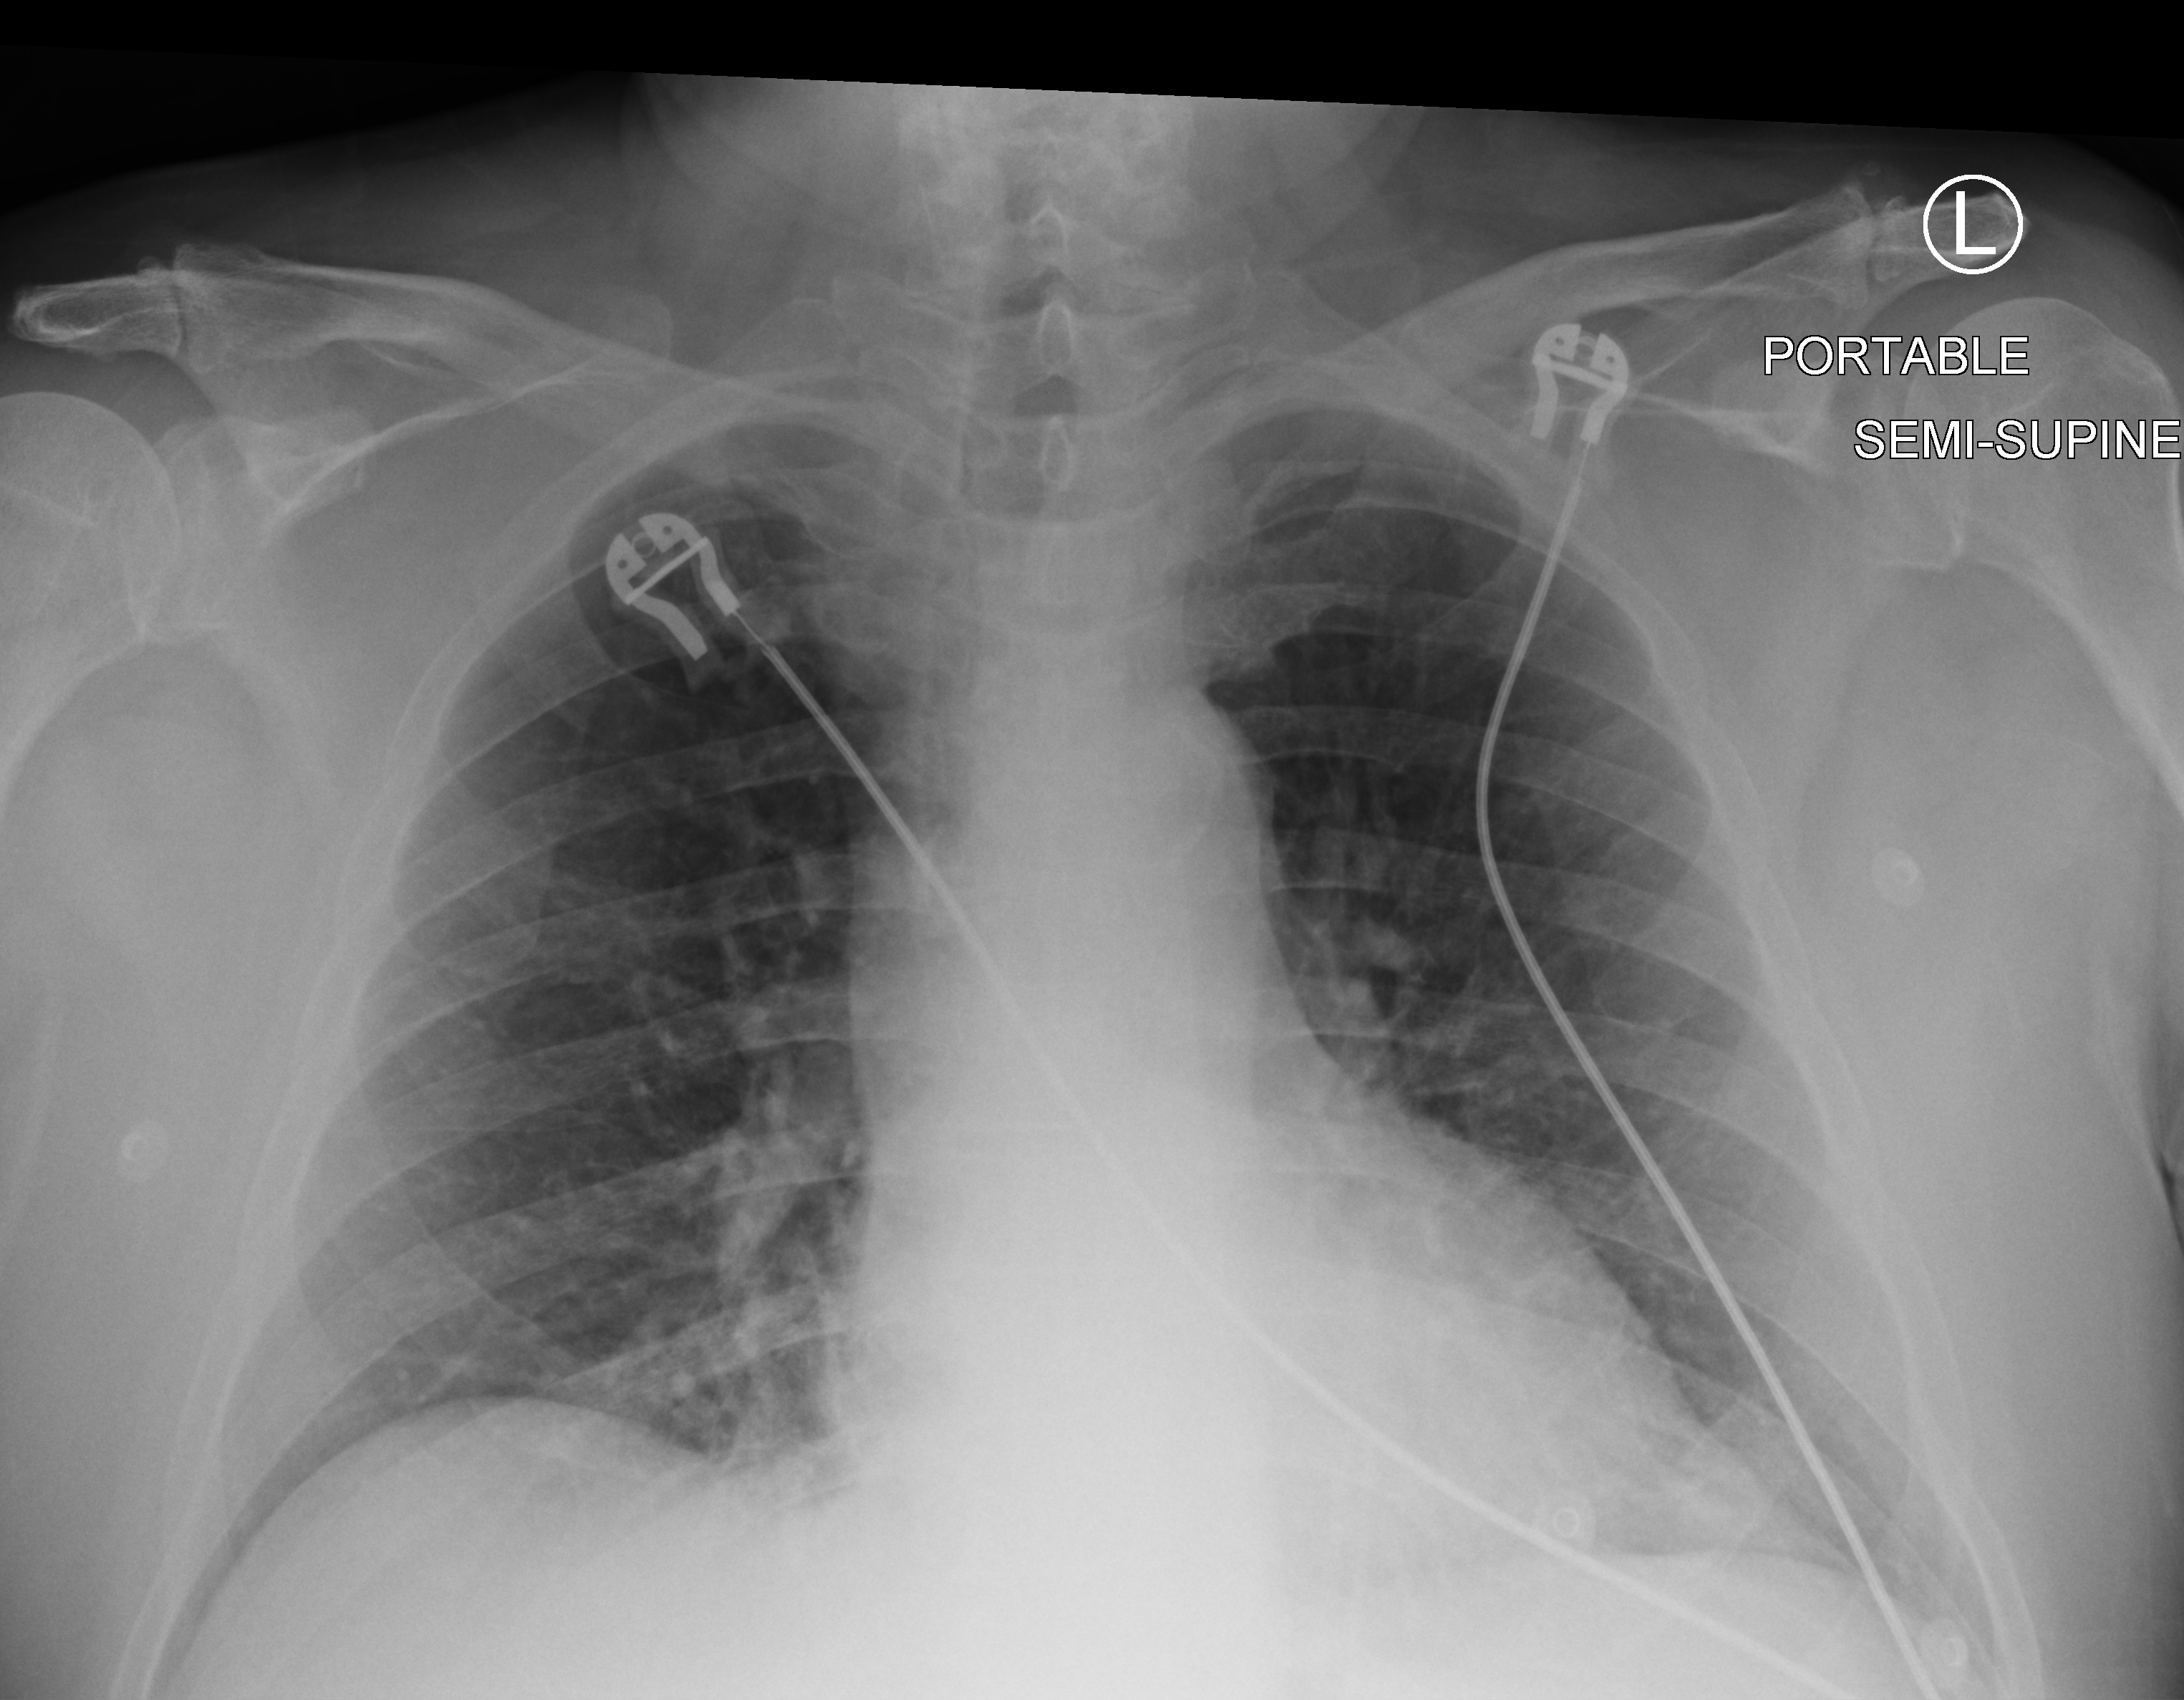
Portable chest radiograph; anteroposterior (AP) projection. Patient hospitalised with COVID-19; male, aged 60–74 years.
Admission-level facts for this patient (not findings on this image; timing relative to this image not recorded):
- mechanically ventilated during this hospital stay: no
- admitted to intensive care during this hospital stay: no